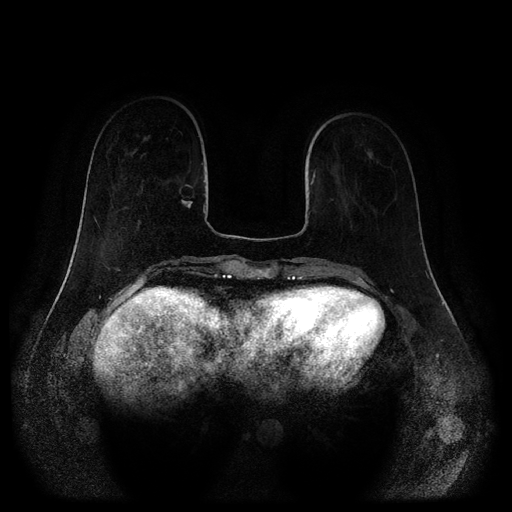
Breast MRI (dynamic contrast-enhanced, multi-phase), one axial slice. Slice 34 of 116 in the series (ordered by position). Dynamic contrast-enhanced series, time point 2 of 5 at this slice position (early post-contrast). 1.5 T. TE 2.6 ms, TR 5.2 ms. 2 mm slice thickness. 512 × 512 image matrix, field of view 380 × 380 mm. Female patient, age 62 years.
Structures marked on this image (semi-automatic segmentation, software-assisted and operator-edited):
- breast lesion (labelled 'tumour' in the annotation; benign lesions carry a separate 'benign' label): bounding box <181,181,195,209> (left, top, right, bottom; pixels)